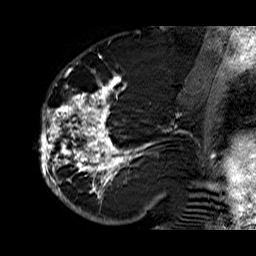
Breast MRI (dynamic contrast-enhanced), one sagittal slice; slice 34 of 60 in the series (ordered by position); dynamic contrast-enhanced series, time point 2 of 6 at this slice position (early post-contrast); 1.5 T; TE 6.3 ms, TR 32.9 ms; 4 mm slice thickness; 256 × 256 image matrix, field of view 200 × 200 mm. Female patient. From the clinical record (not read from this slice): setting: breast cancer imaged before/during neoadjuvant chemotherapy; receptor status: HR-positive, HER2-negative.
Outlined on this slice (semi-automatic segmentation, software-assisted and operator-edited):
- analysis volume of interest (the breast-tissue region the enhancement analysis was run in; not a lesion): bounding box (x1, y1, x2, y2) in pixels: (39, 74, 176, 210)
- tumour enhancement mask (voxels above the 100 % enhancement threshold inside the analysis volume of interest): (39, 74, 153, 210)